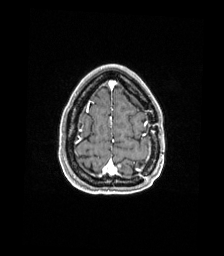
Brain MRI from a brain-tumour surgery series, one axial slice; slice 37 of 176 in the series (ordered by position); T1-weighted post-contrast; 1 mm slice thickness; 224 × 256 image matrix, field of view 224 × 256 mm. Case-level facts recorded for this patient, not image findings: histopathology: Atypical meningioma; WHO grade: 2; tumour location: Paramedian Left Parietal.
Outlined on this slice (manually delineated by an expert):
- previous resection cavity: bounding box (x1, y1, x2, y2) in pixels: (139, 163, 142, 165)
- tumour: (117, 163, 122, 168)